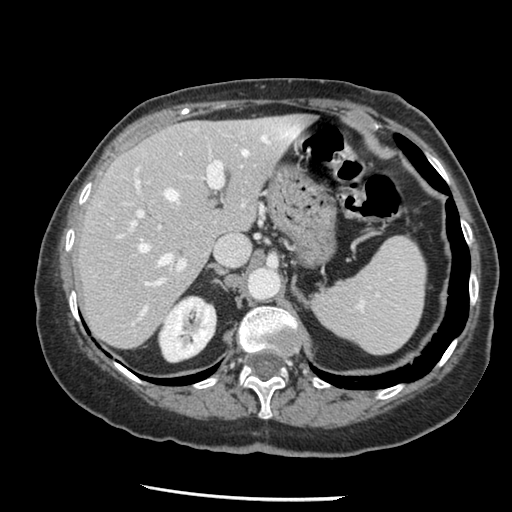
Contrast-enhanced abdominal CT, one axial slice. Slice 92 of 148 in the series (ordered by position). Reconstruction kernel STANDARD. Intravenous contrast given. Soft-tissue window (W 400 / L 40 HU). 2.5 mm slice thickness. 512 × 512 image matrix. Female patient, age 85 years. Case-level facts recorded for this patient, not image findings: diagnosis: colorectal cancer liver metastases, imaged before liver resection; multiple liver metastases: no; largest metastasis: 0.9 cm; chemotherapy before resection: yes.
Annotated regions visible in this slice (expert manual segmentation):
- hepatic veins: bounding box (x1, y1, x2, y2) in pixels: (139, 133, 297, 314)
- liver: (80, 116, 312, 348)
- planned liver remnant (the part of the liver to remain after resection): (80, 116, 312, 348)
- portal vein (with intrahepatic branches): (117, 141, 224, 286)